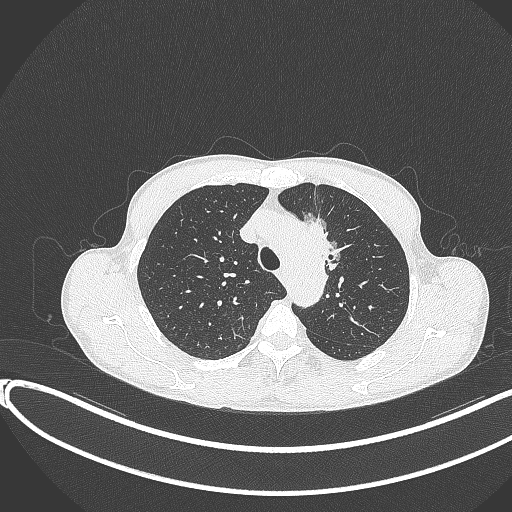
Chest CT, one axial slice; position 289 of 374 along the scan axis; 120 kVp; lung window (W 1500 / L -600 HU); 1 mm slice thickness; 512 × 512 image matrix, field of view 400 × 400 mm. Patient: male, 58 years. Case-level facts recorded for this patient, not image findings: clinical TNM (as recorded): T1c N1 M0.
Outlined on this slice (bounding box drawn by a radiologist):
- lung tumour (recorded histology: adenocarcinoma): bounding box [x1, y1, x2, y2] px = [298, 205, 348, 277]